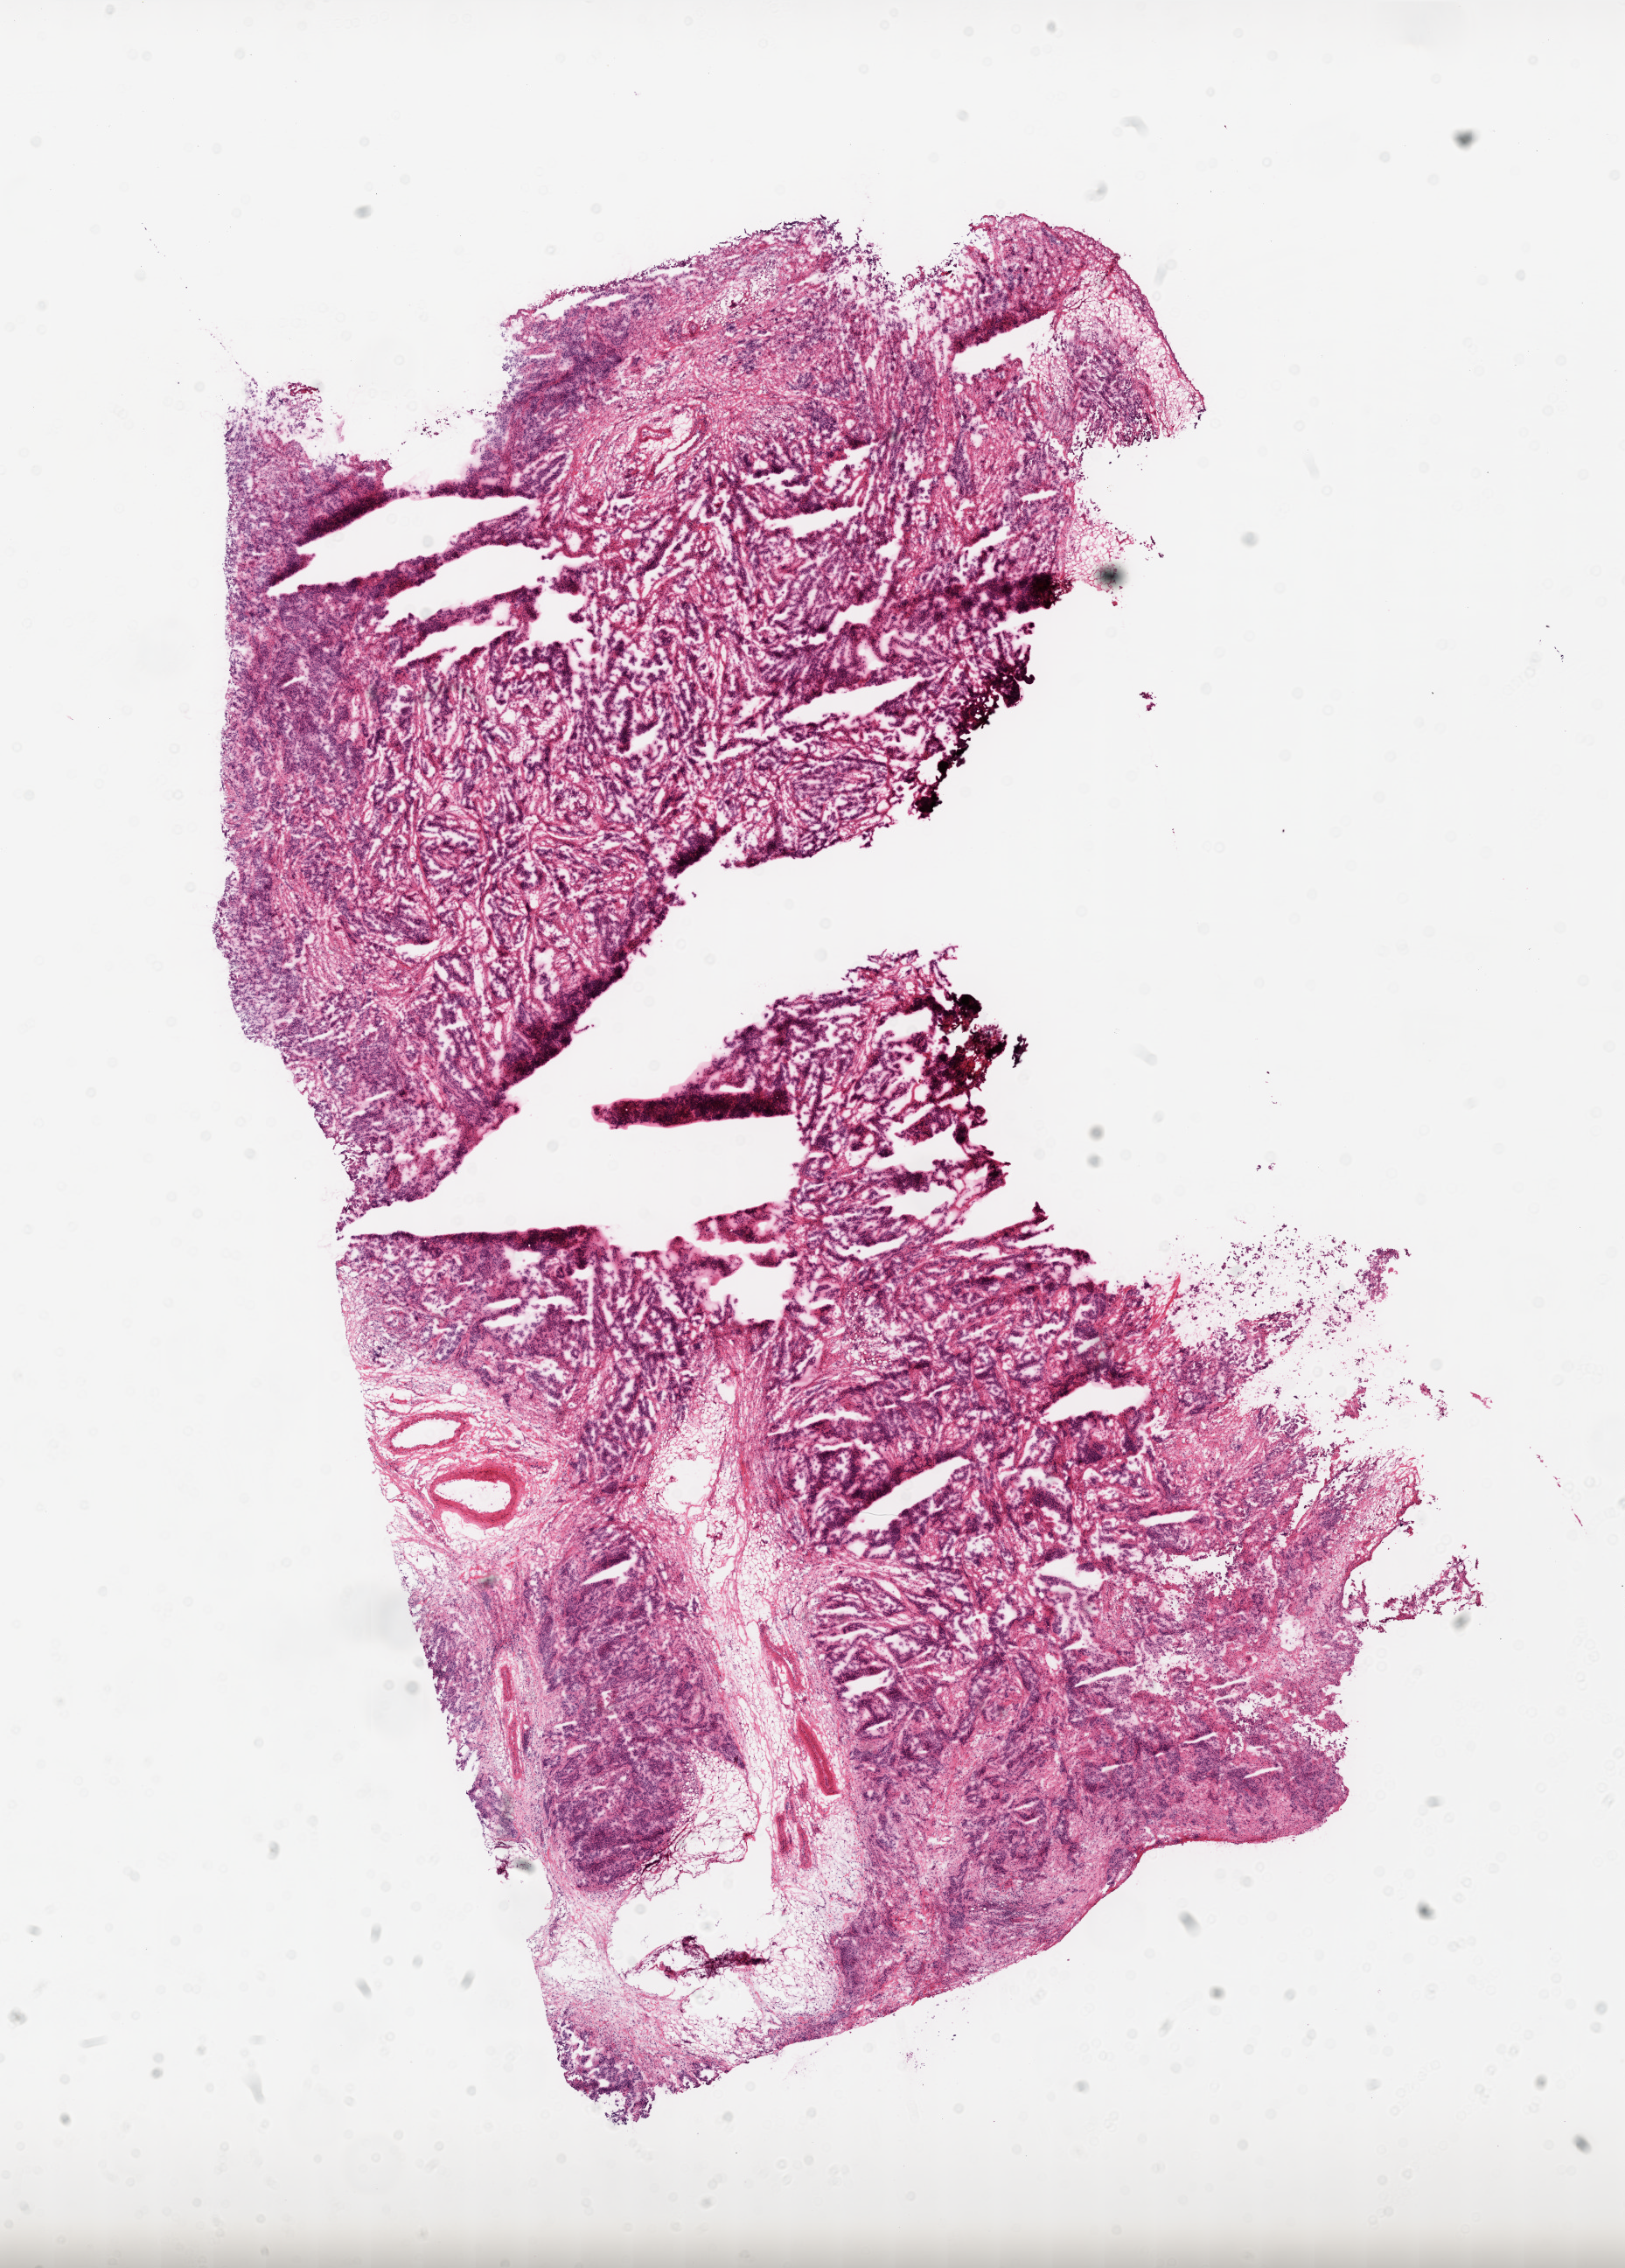
Hematoxylin and eosin (H&E) stained whole-slide image — low-resolution overview of the scanned area, about 14.9 x 20.9 mm (acquisition: 20x scan), frozen section, ovary, primary tumour sample. Female, age 40 years at initial diagnosis. Histologic grade: G3 (poorly differentiated). Pathologist review of this section (percent, as recorded): tumour cells 80%, tumour nuclei 90%, normal cells 0%, stromal cells 20%, necrosis 0%.
Diagnosis: Serous cystadenocarcinoma, NOS. FIGO stage: IV.